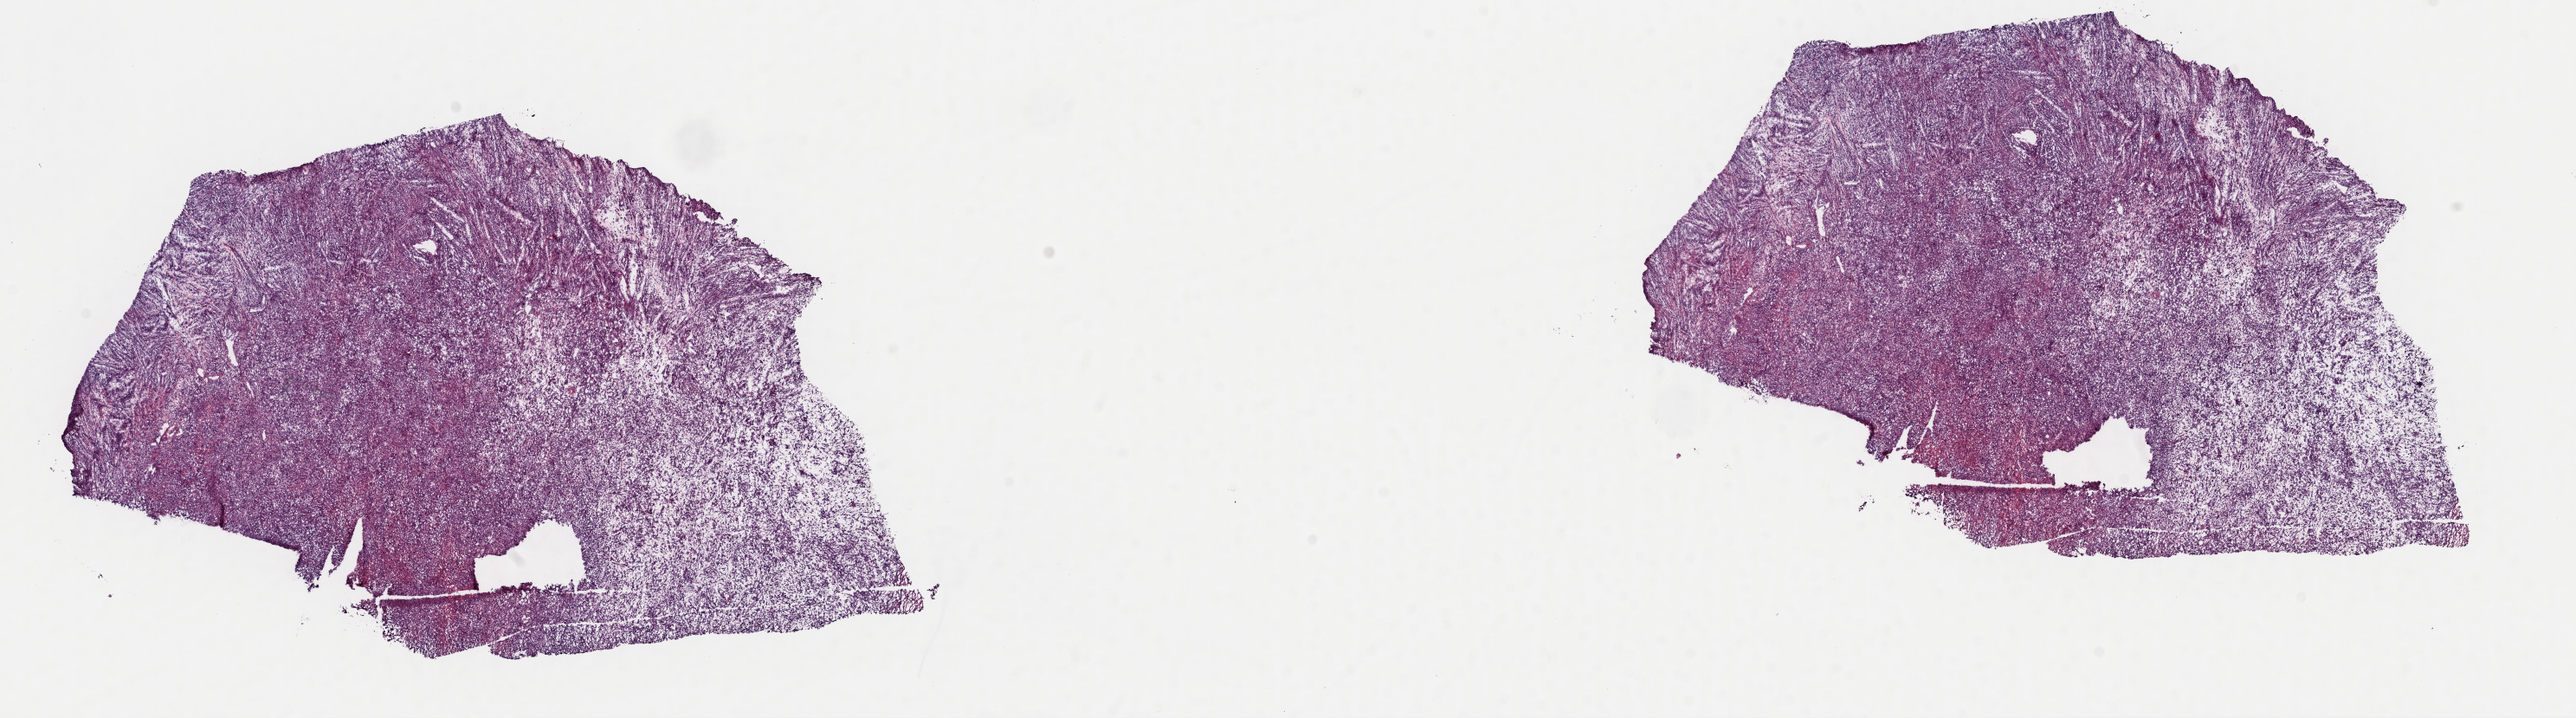
Whole-slide histology image, H&E, shown as a low-resolution overview of the whole scanned area (about 23.5 x 6.5 mm), frozen section from the top of the tissue portion, retroperitoneum and peritoneum, primary tumour sample. Female patient; age at initial diagnosis 85 years. Slide review estimates, as recorded: tumour cells 100%, tumour nuclei 80%, normal cells 0%, stromal cells 0%, necrosis 0%. Inflammatory infiltration, as recorded: lymphocyte infiltration 1%, monocyte infiltration 0%, neutrophil infiltration 0%.
Histologic diagnosis: Dedifferentiated liposarcoma (retroperitoneum).